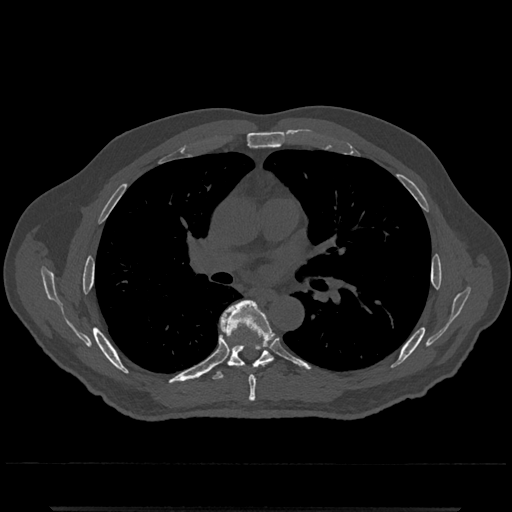
CT including the spine, one axial slice; 120 kVp; bone window (W 1800 / L 400 HU); 0.5 mm slice thickness; 512 × 512 image matrix. Patient: male, 67 years. Case-level facts recorded for this patient, not image findings: primary cancer: prostate.
Annotated regions visible in this slice (semi-automatically segmented with operator editing):
- T6 vertebra: box from (x=222, y=300) to (x=274, y=402) px
- T7 vertebra: (x=210, y=331)–(x=273, y=380)